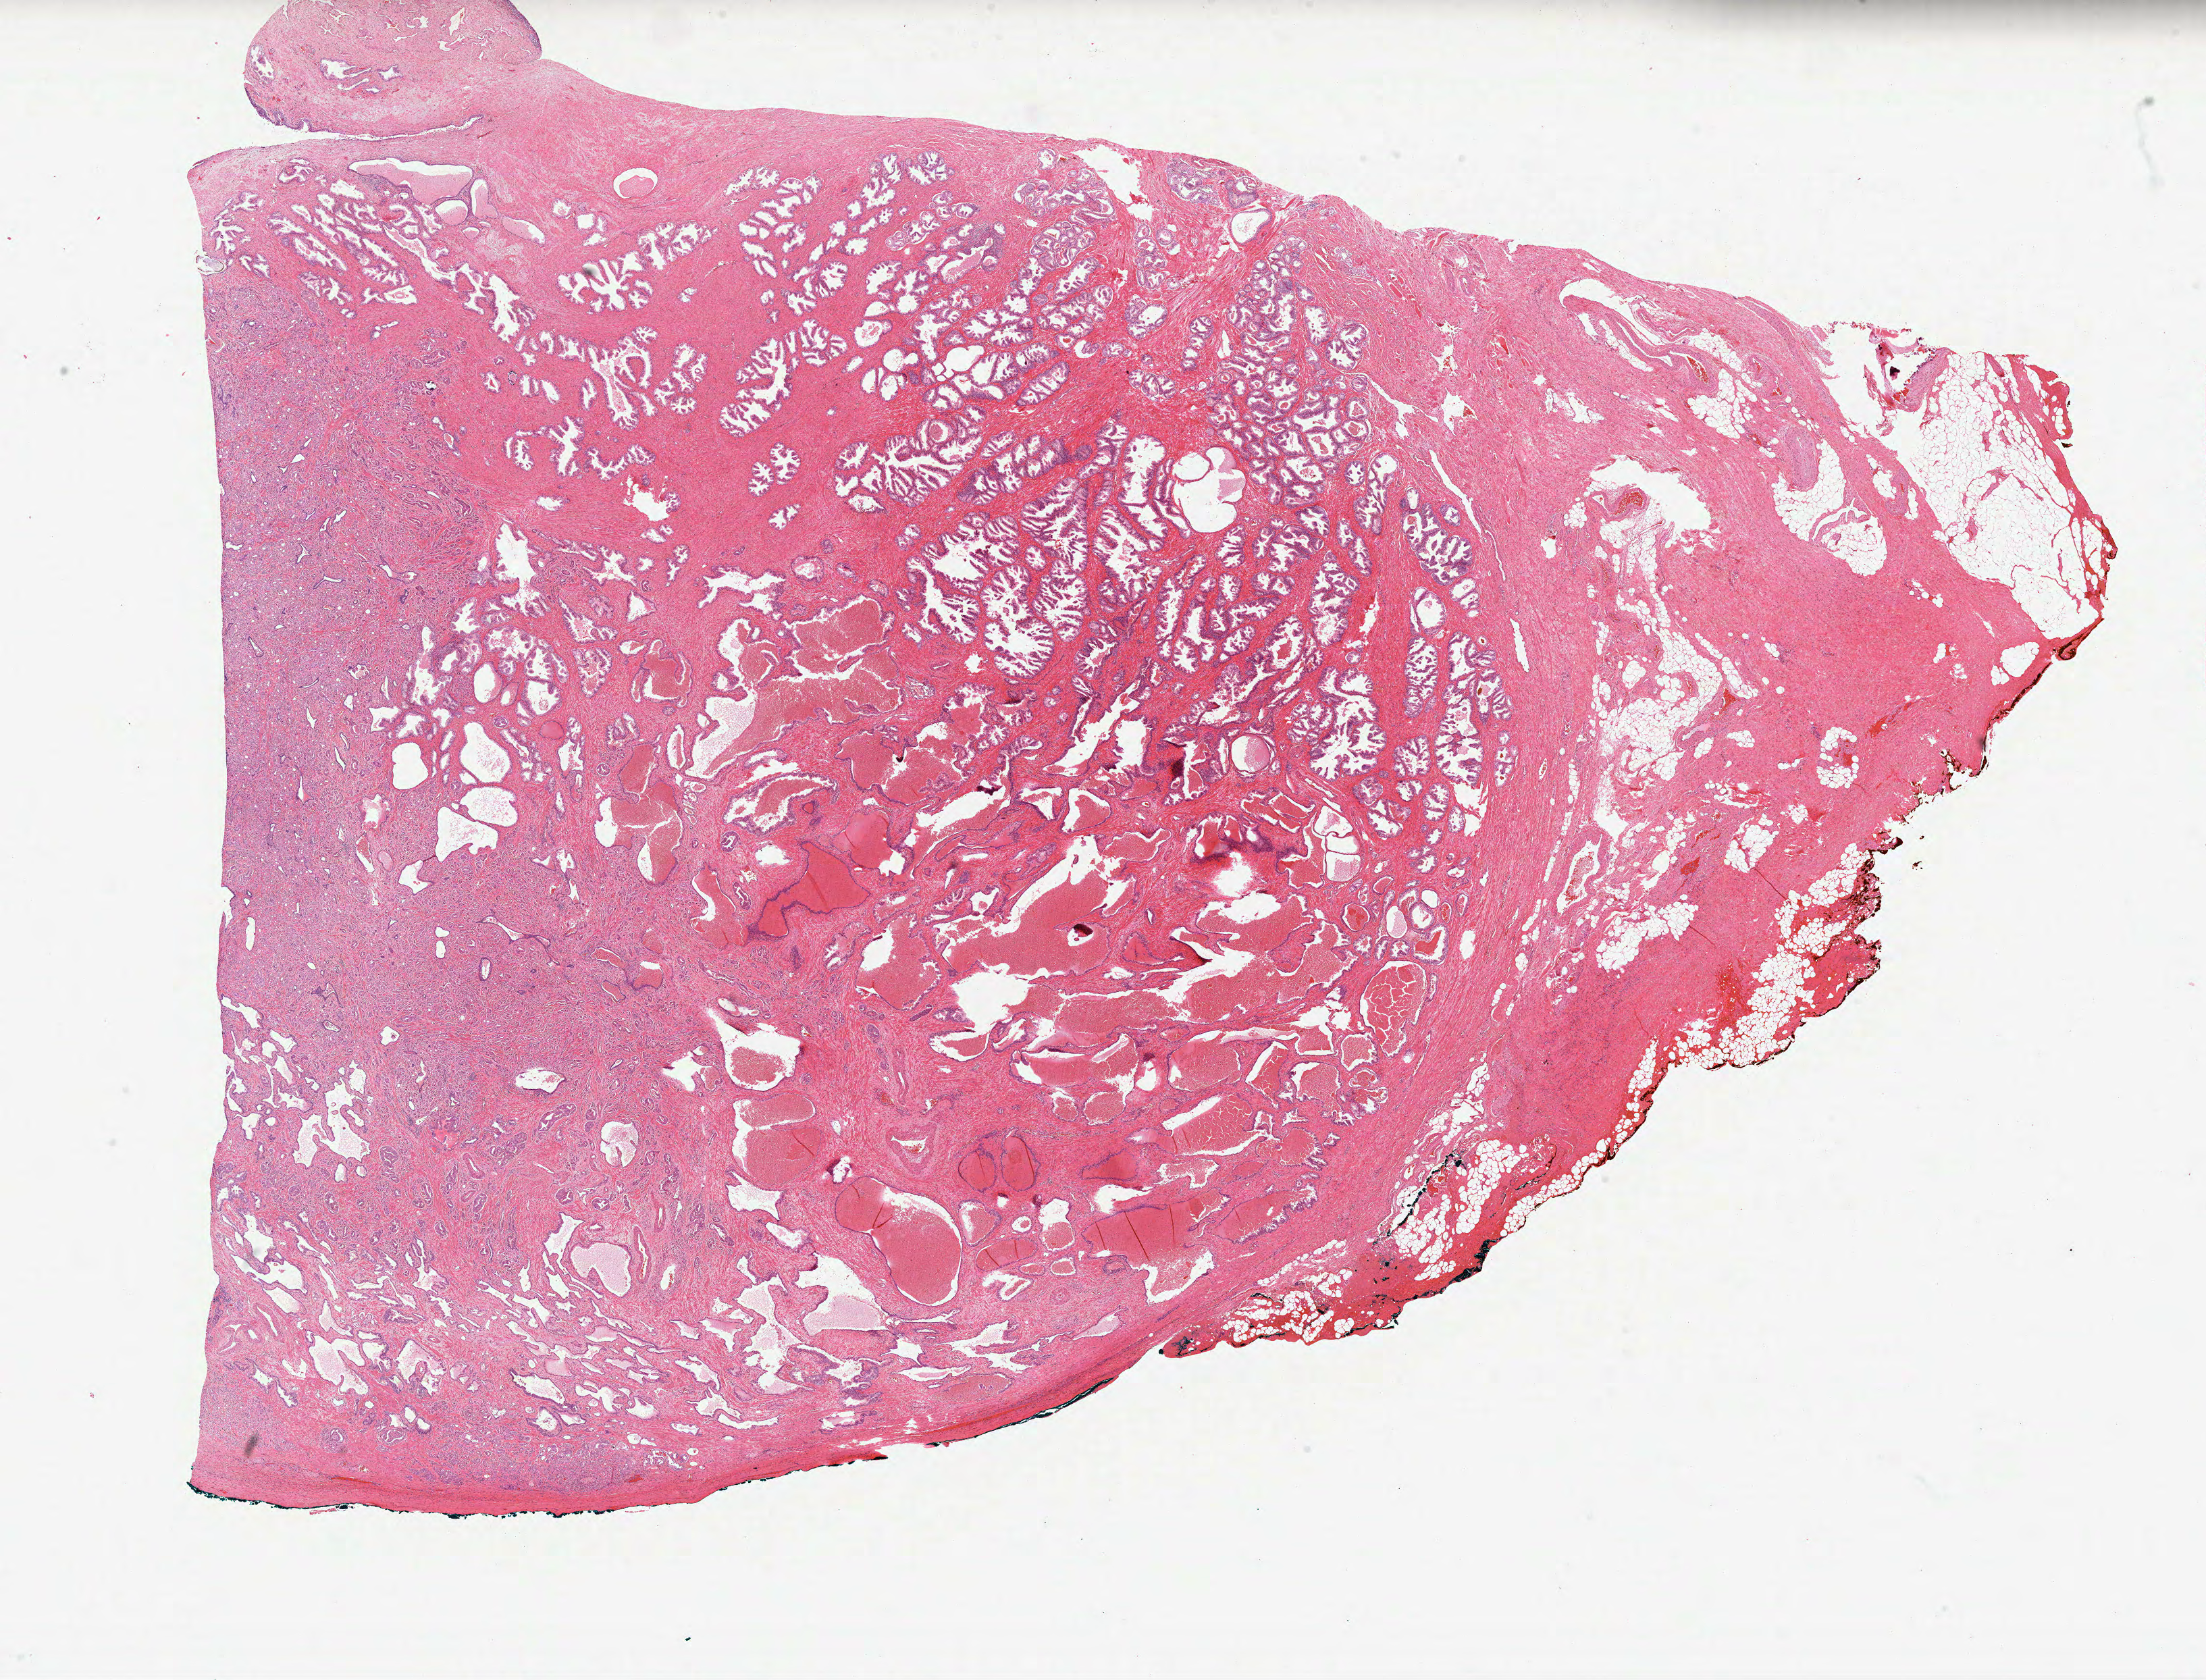
Hematoxylin and eosin (H&E) stained whole-slide image — a low-resolution overview of the entire scanned area, about 26.3 x 20.1 mm (slide scanned at 40x), formalin-fixed paraffin-embedded (FFPE) diagnostic section, primary tumour sample from the prostate. Male, age 68 years at initial diagnosis. Gleason score: 7 (3+4).
Pathologic diagnosis: Acinar cell carcinoma (prostate gland). Lymph nodes positive (case pathology): 0 of 15 examined. Laterality: bilateral.